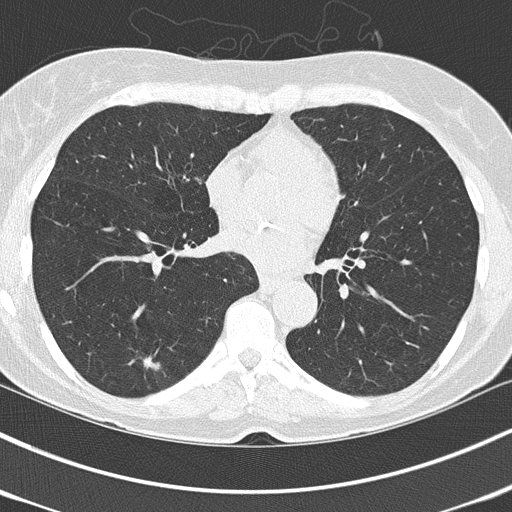
Chest CT (low-dose screening protocol), one axial image; third annual screen; lung window (W 1500 / L -600 HU); 2 mm slice thickness; lung (sharp) reconstruction kernel (B50f); 512 × 512 image matrix, field of view 318 × 318 mm. Female, age 67 years at enrolment. Current smoker at enrolment.
Expert-annotated lung lesion, box from (x=129, y=347) to (x=167, y=381) px. The screening reader recorded 3 non-calcified nodules or masses ≥4 mm on this exam (right lower lobe, right lower lobe, left lower lobe); which of them this box marks is not recorded. Official screen result: positive, other. Lung cancer was diagnosed 64 days after this screen: adenocarcinoma, NOS, left lower lobe, poorly differentiated (G3), stage IA (AJCC 6th edition), 25 mm at pathology.